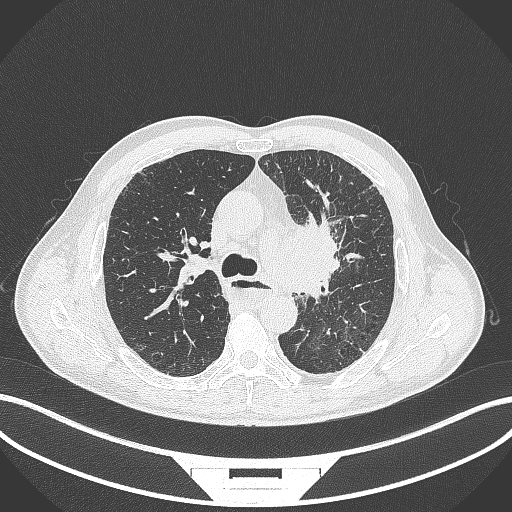
Chest CT, one axial slice; slice 254 of 411 in the series (ordered by position); reconstruction kernel B70f; lung window (W 1500 / L -600 HU); 1 mm slice thickness; 512 × 512 image matrix. Male patient, age 57 years. Case-level facts recorded for this patient, not image findings: clinical TNM (as recorded): T2a N1 M0.
Annotated regions visible in this slice (rectangle marked by the reading radiologist):
- lung tumour (recorded histology: squamous cell carcinoma): bounding box <279,214,345,313> (left, top, right, bottom; pixels)